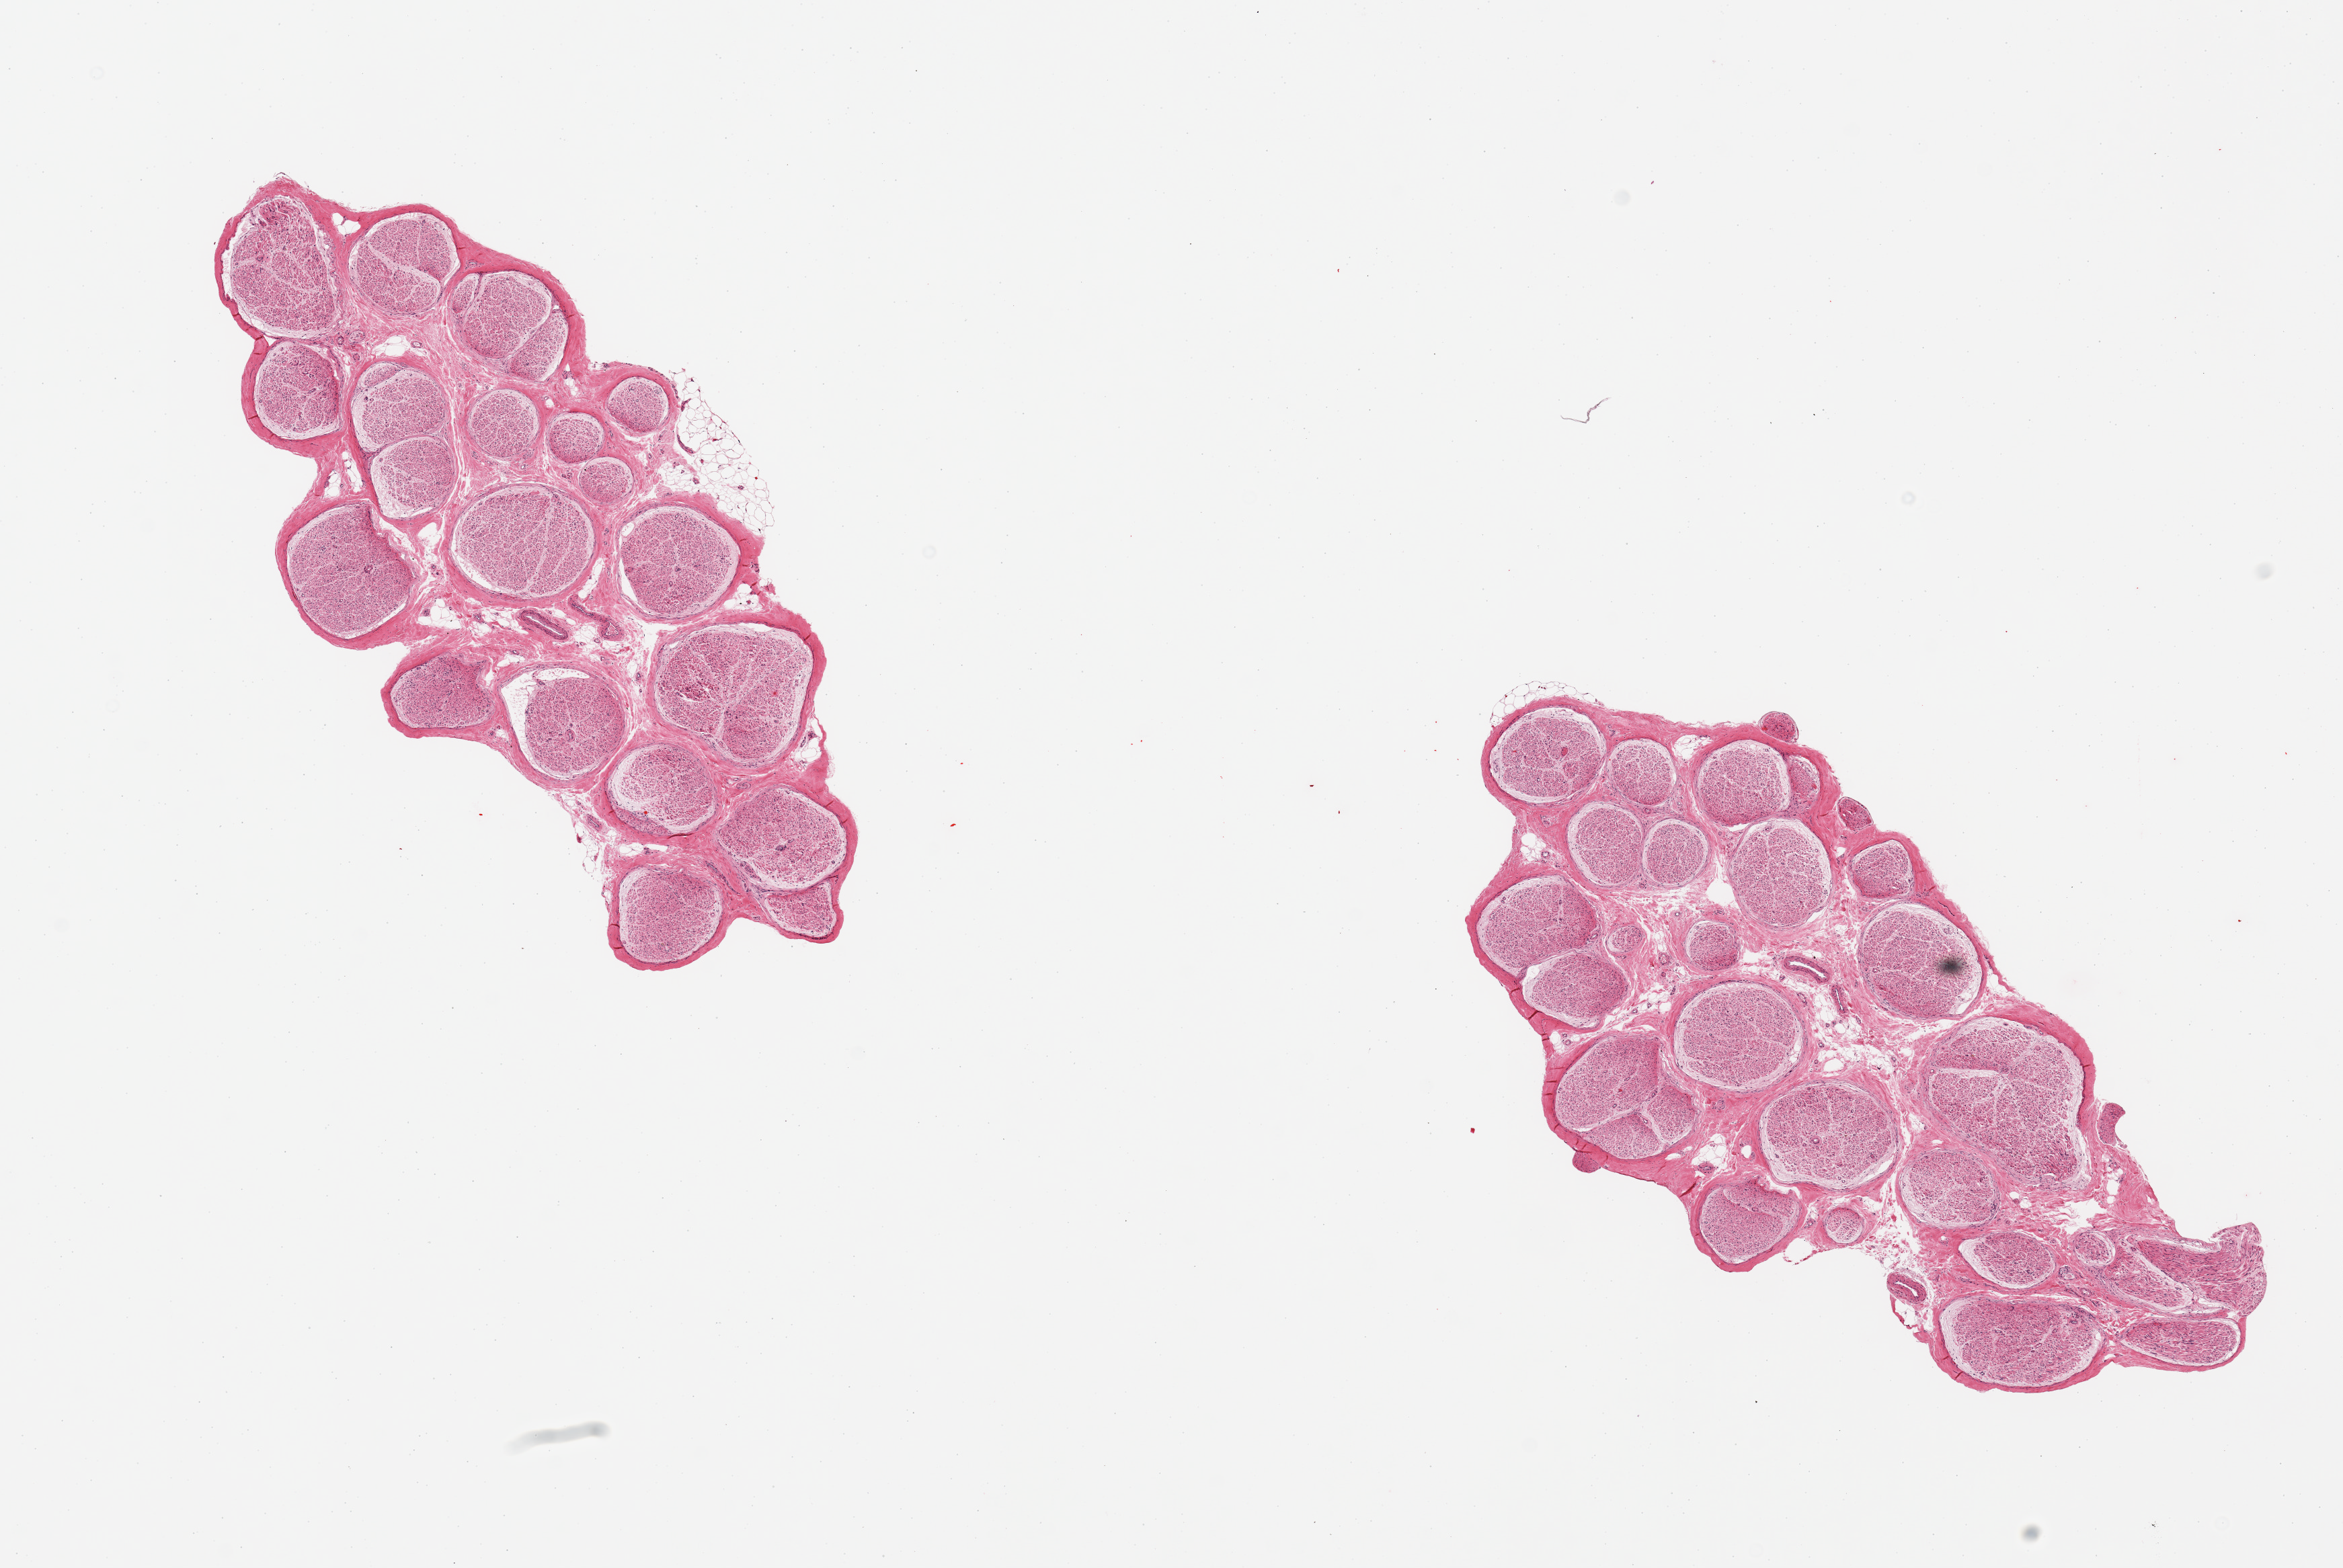
Whole-slide image, H&E stain — a low-resolution overview of the entire scanned area, about 13.8 x 9.2 mm, PAXgene-fixed paraffin-embedded (PFPE) section, sampled site (target tissue): tibial nerve, donor tissue sample. Donor: male.
Pathologist's review note for this sample: 2 pieces, minimal adherent fat, good aliquots.